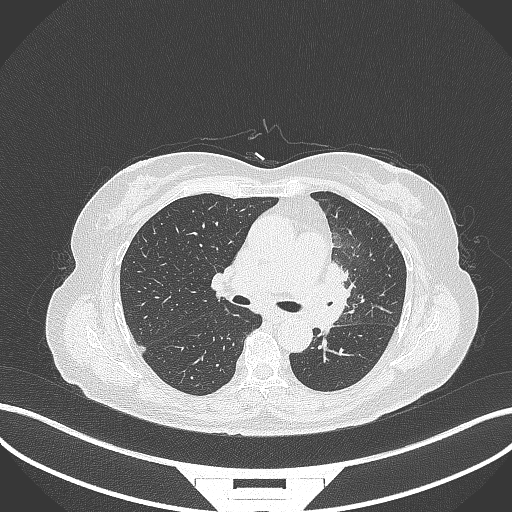
Chest CT, one axial slice. Position 199 of 382 along the scan axis. Reconstruction kernel B70f. 120 kVp. Lung window (W 1500 / L -600 HU). 1 mm slice thickness. 512 × 512 image matrix. Patient: female, 64 years. Case-level facts recorded for this patient, not image findings: clinical TNM (as recorded): T2a N2 M0.
Outlined on this slice (bounding box drawn by a radiologist):
- lung tumour (recorded histology: adenocarcinoma): bounding box <320,253,358,333> (left, top, right, bottom; pixels)